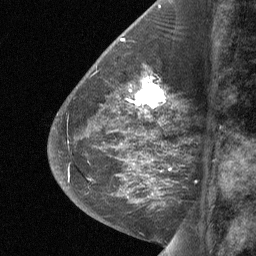
Breast MRI (dynamic contrast-enhanced), one sagittal slice; position 27 of 64 along the scan axis; dynamic contrast-enhanced study with each time point stored as its own series, time point 2 of 3 at this slice position (early post-contrast, ordered by acquisition time); 1.5 T; TE 4.8 ms, TR 27 ms; 2 mm slice thickness; 256 × 256 image matrix, field of view 180 × 180 mm. Female patient, age 59 years. Case-level facts recorded for this patient, not image findings: setting: breast cancer imaged before/during neoadjuvant chemotherapy; receptor status: triple-negative.
Annotated regions visible in this slice (semi-automatic segmentation, software-assisted and operator-edited):
- analysis volume of interest (the breast-tissue region the enhancement analysis was run in; not a lesion): bounding box <126,75,173,114> (left, top, right, bottom; pixels)
- tumour enhancement mask (voxels above the 90 % enhancement threshold inside the analysis volume of interest): <129,76,166,110>